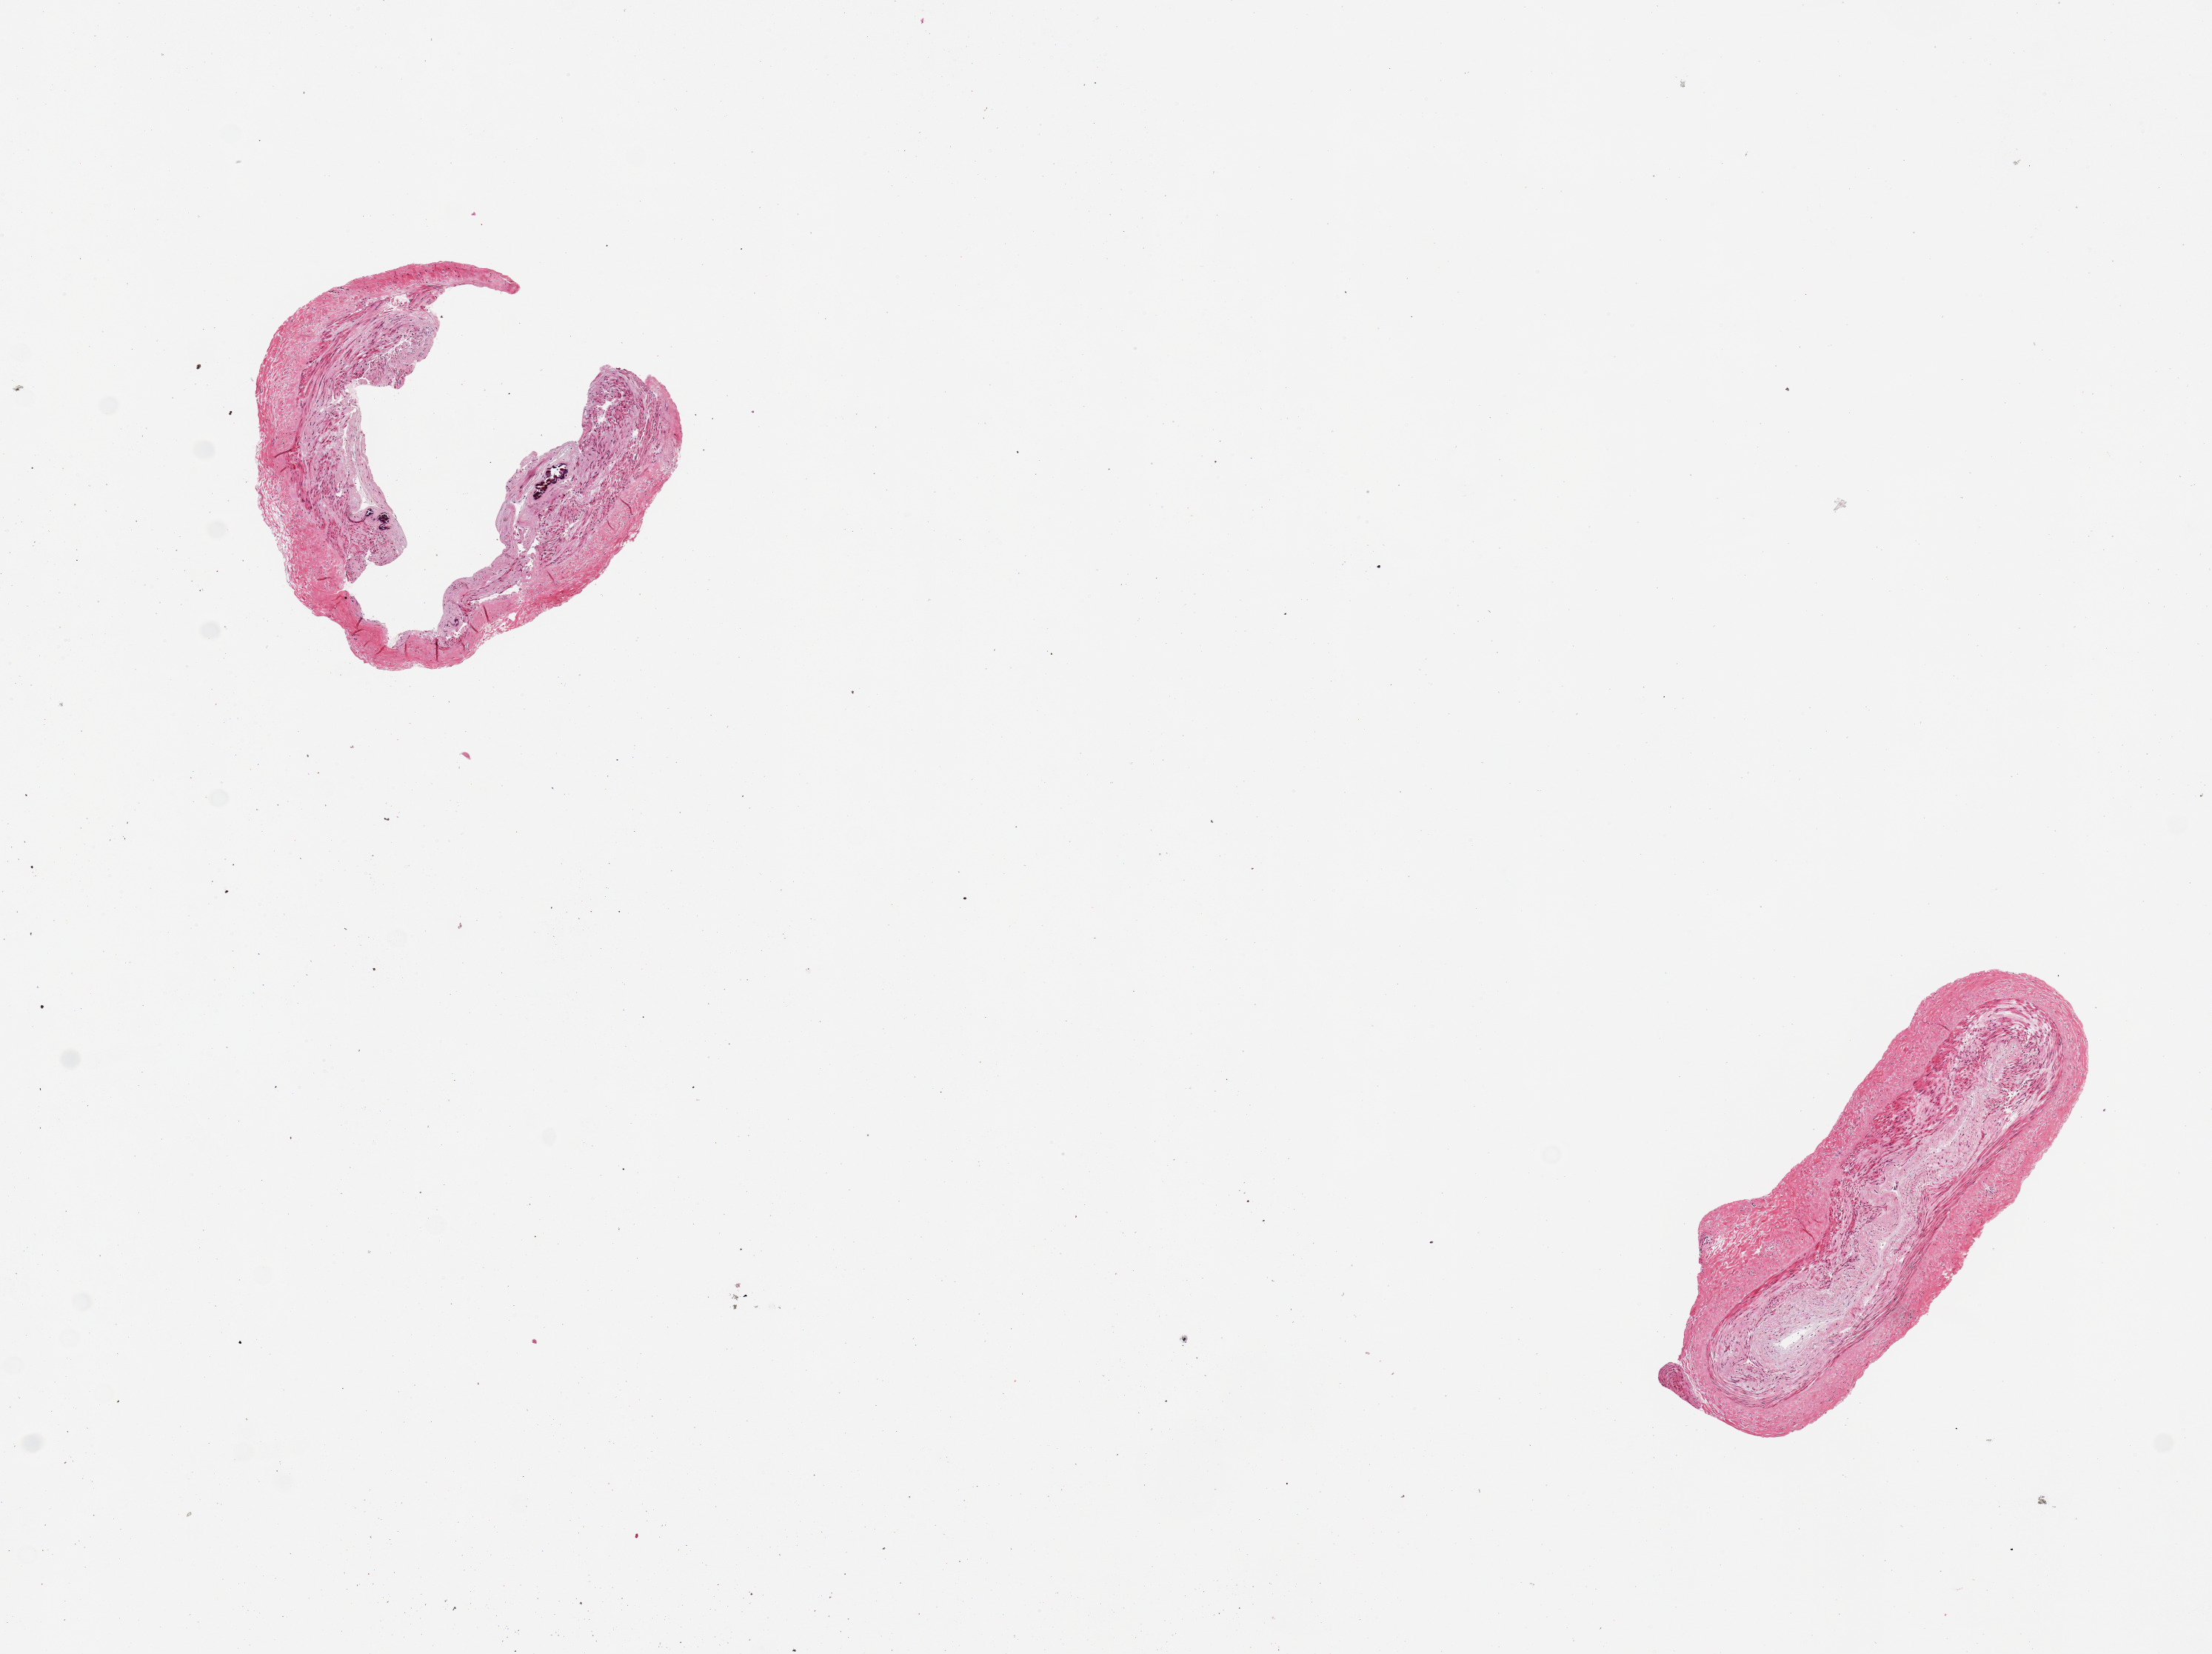
Whole-slide image, hematoxylin and eosin (H&E) stain — whole scanned area (about 11.8 x 8.8 mm) shown as a low-resolution overview. PAXgene-fixed, paraffin-embedded tissue. Target tissue: tibial artery. Donor tissue sample. Female donor.
Review note (as recorded): 2 pieces, 2x2 & 3x1mm; intimal fibrosis and in one, focal calcification.